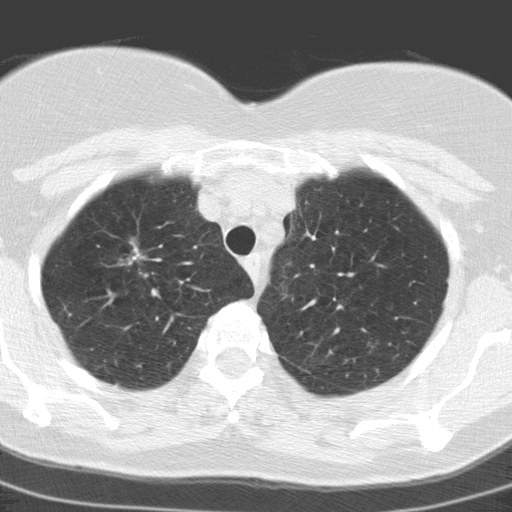
Axial slice from a low-dose chest CT screening exam. Baseline annual screen. Lung window (W 1500 / L -600 HU). 3.2 mm slice thickness. Standard (soft-tissue) reconstruction kernel (C). 512 × 512 image matrix. Female, age 60 years at enrolment. Former smoker at enrolment.
Lesion marked by an expert reader, box from (x=101, y=233) to (x=159, y=280) px. No non-calcified nodule or mass ≥4 mm was recorded by the screening reader at this exam. Later outcome: lung cancer diagnosed 447 days after this screen (after the second annual screen) — adenocarcinoma, NOS, right upper lobe, moderately differentiated (G2), stage IA (AJCC 6th edition), 23 mm at pathology.